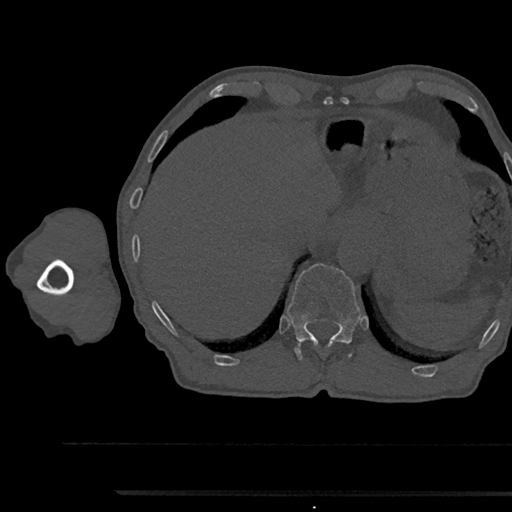
CT including the spine, one axial slice; slice 739 of 797 in the series (ordered by position); reconstruction kernel Br40s/3; bone window (W 1800 / L 400 HU); 512 × 512 image matrix, field of view 367 × 367 mm. Male patient, age 79 years. From the clinical record (not read from this slice): primary cancer: prostate.
Outlined on this slice (semi-automatic segmentation, software-assisted and operator-edited):
- T12 vertebra: bounding box <287,263,360,360> (left, top, right, bottom; pixels)